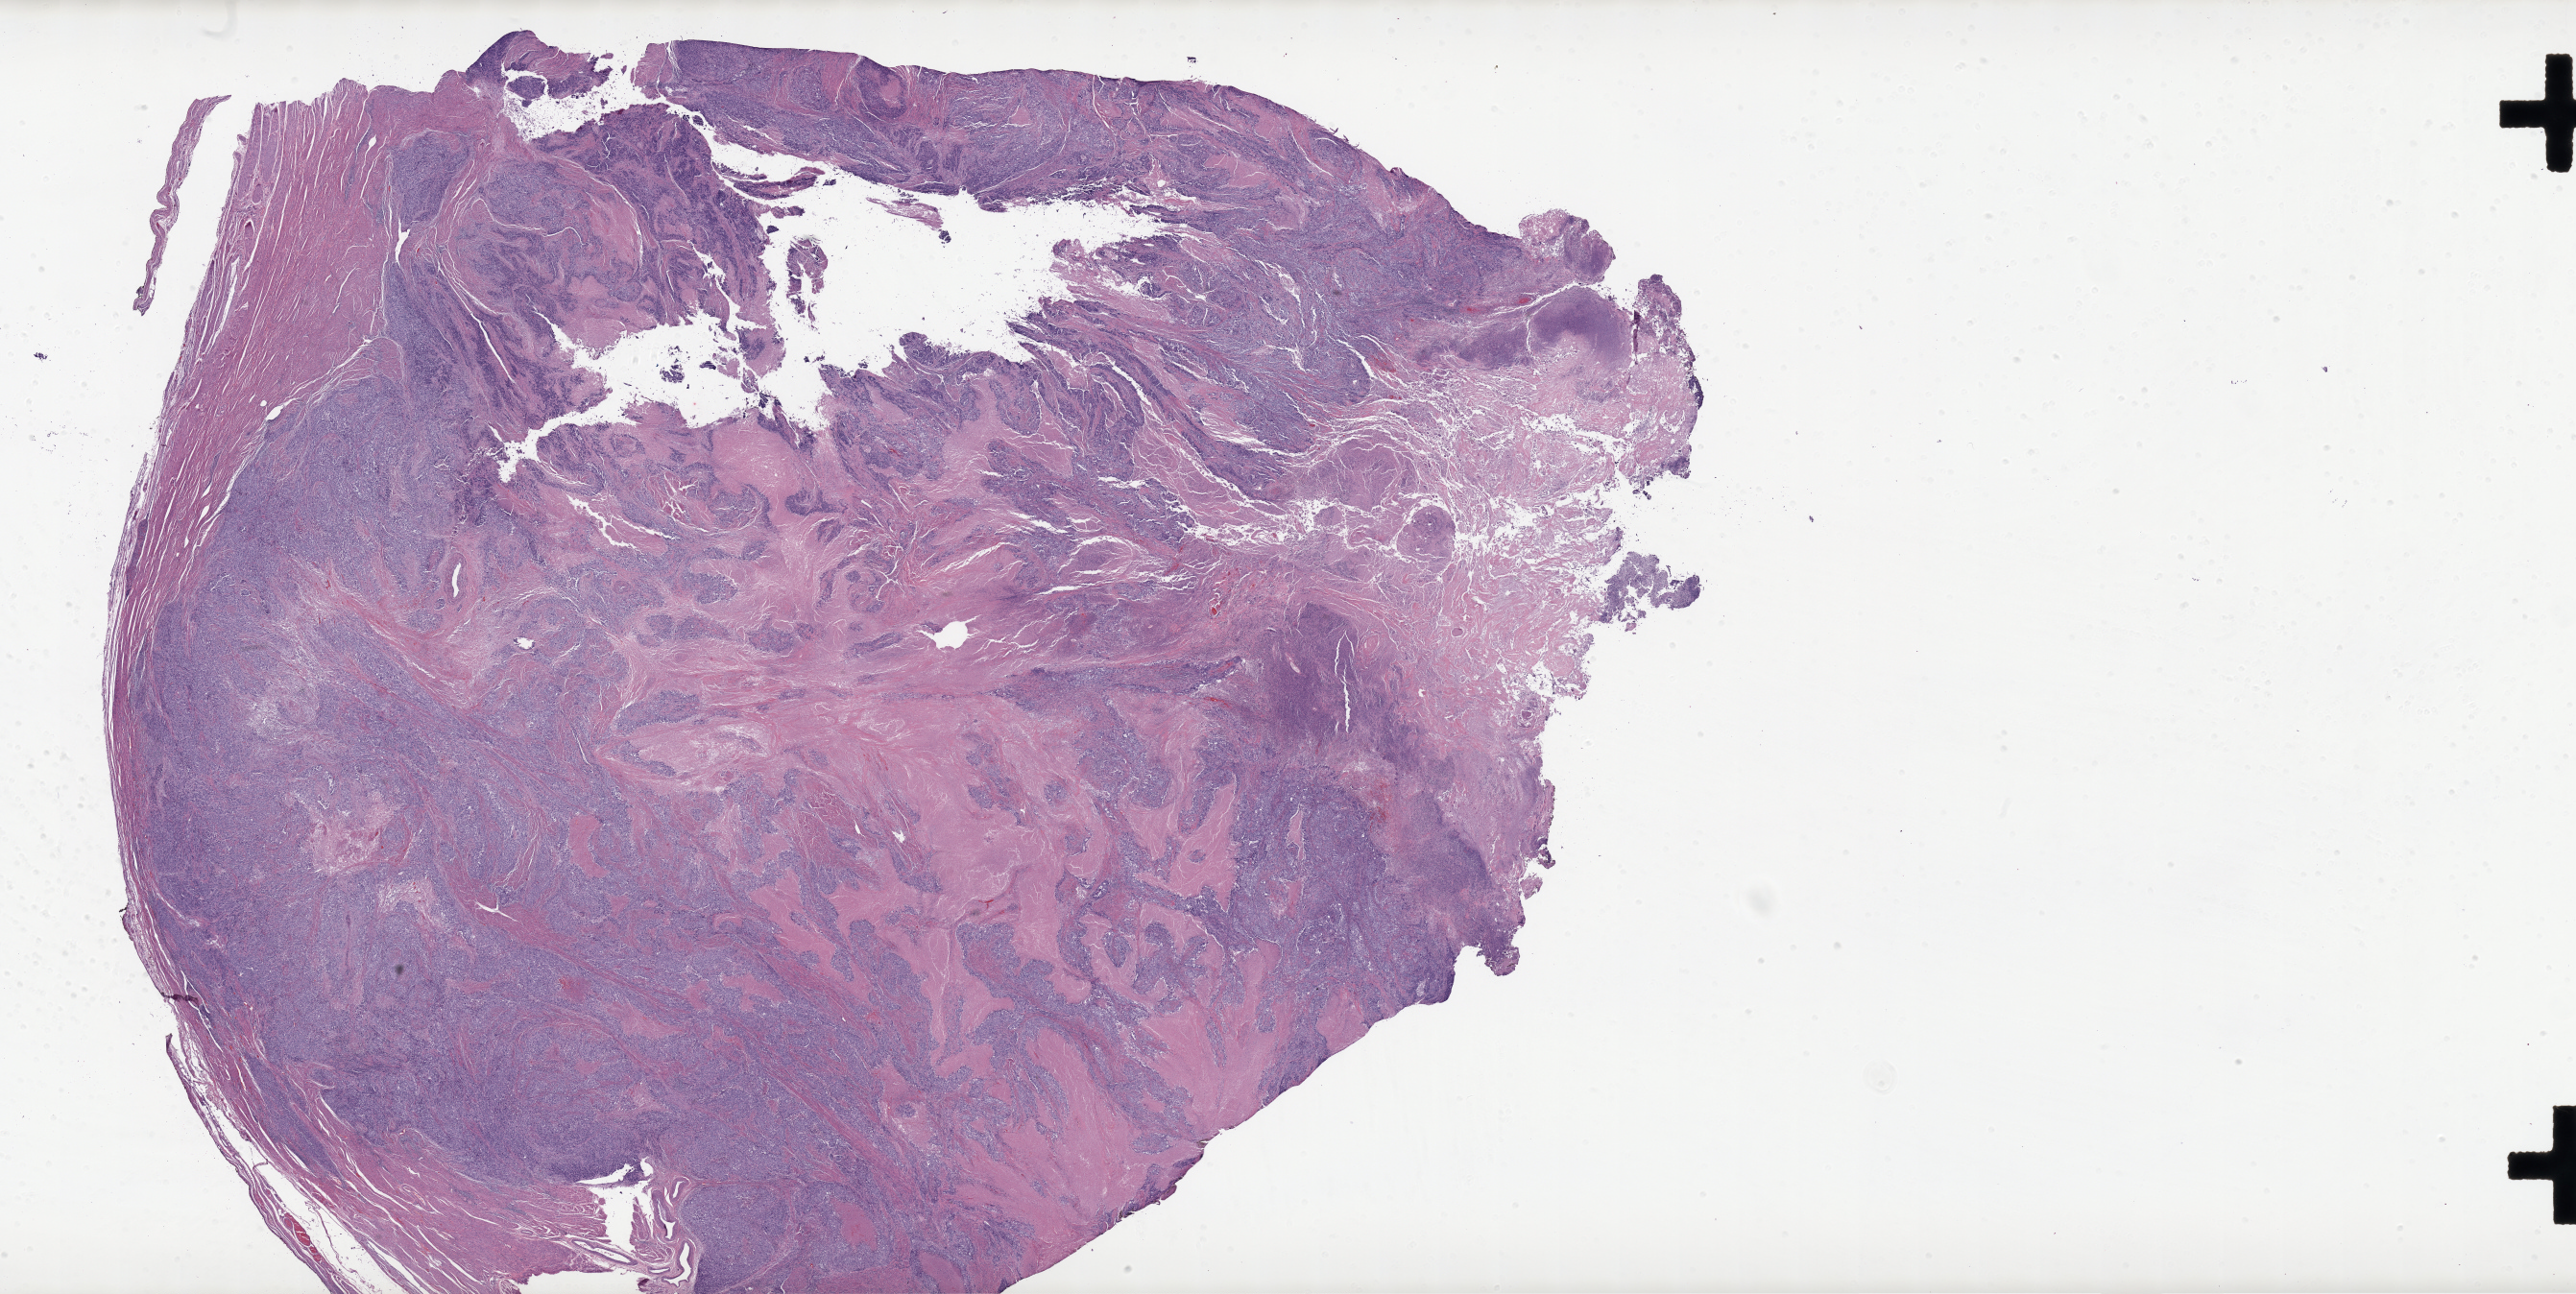
Whole-slide histology image, H&E — low-resolution overview of the scanned area, about 42.8 x 21.5 mm (acquisition: 20x scan). Formalin-fixed paraffin-embedded (FFPE) diagnostic section. Uterus, primary tumour sample. Patient: female, age at initial diagnosis 64 years. Histologic grade: G3 (poorly differentiated).
• pathologic diagnosis: Endometrioid adenocarcinoma, NOS (endometrium)
• lymph nodes positive (case pathology): 0 of 20 examined
• FIGO stage: II